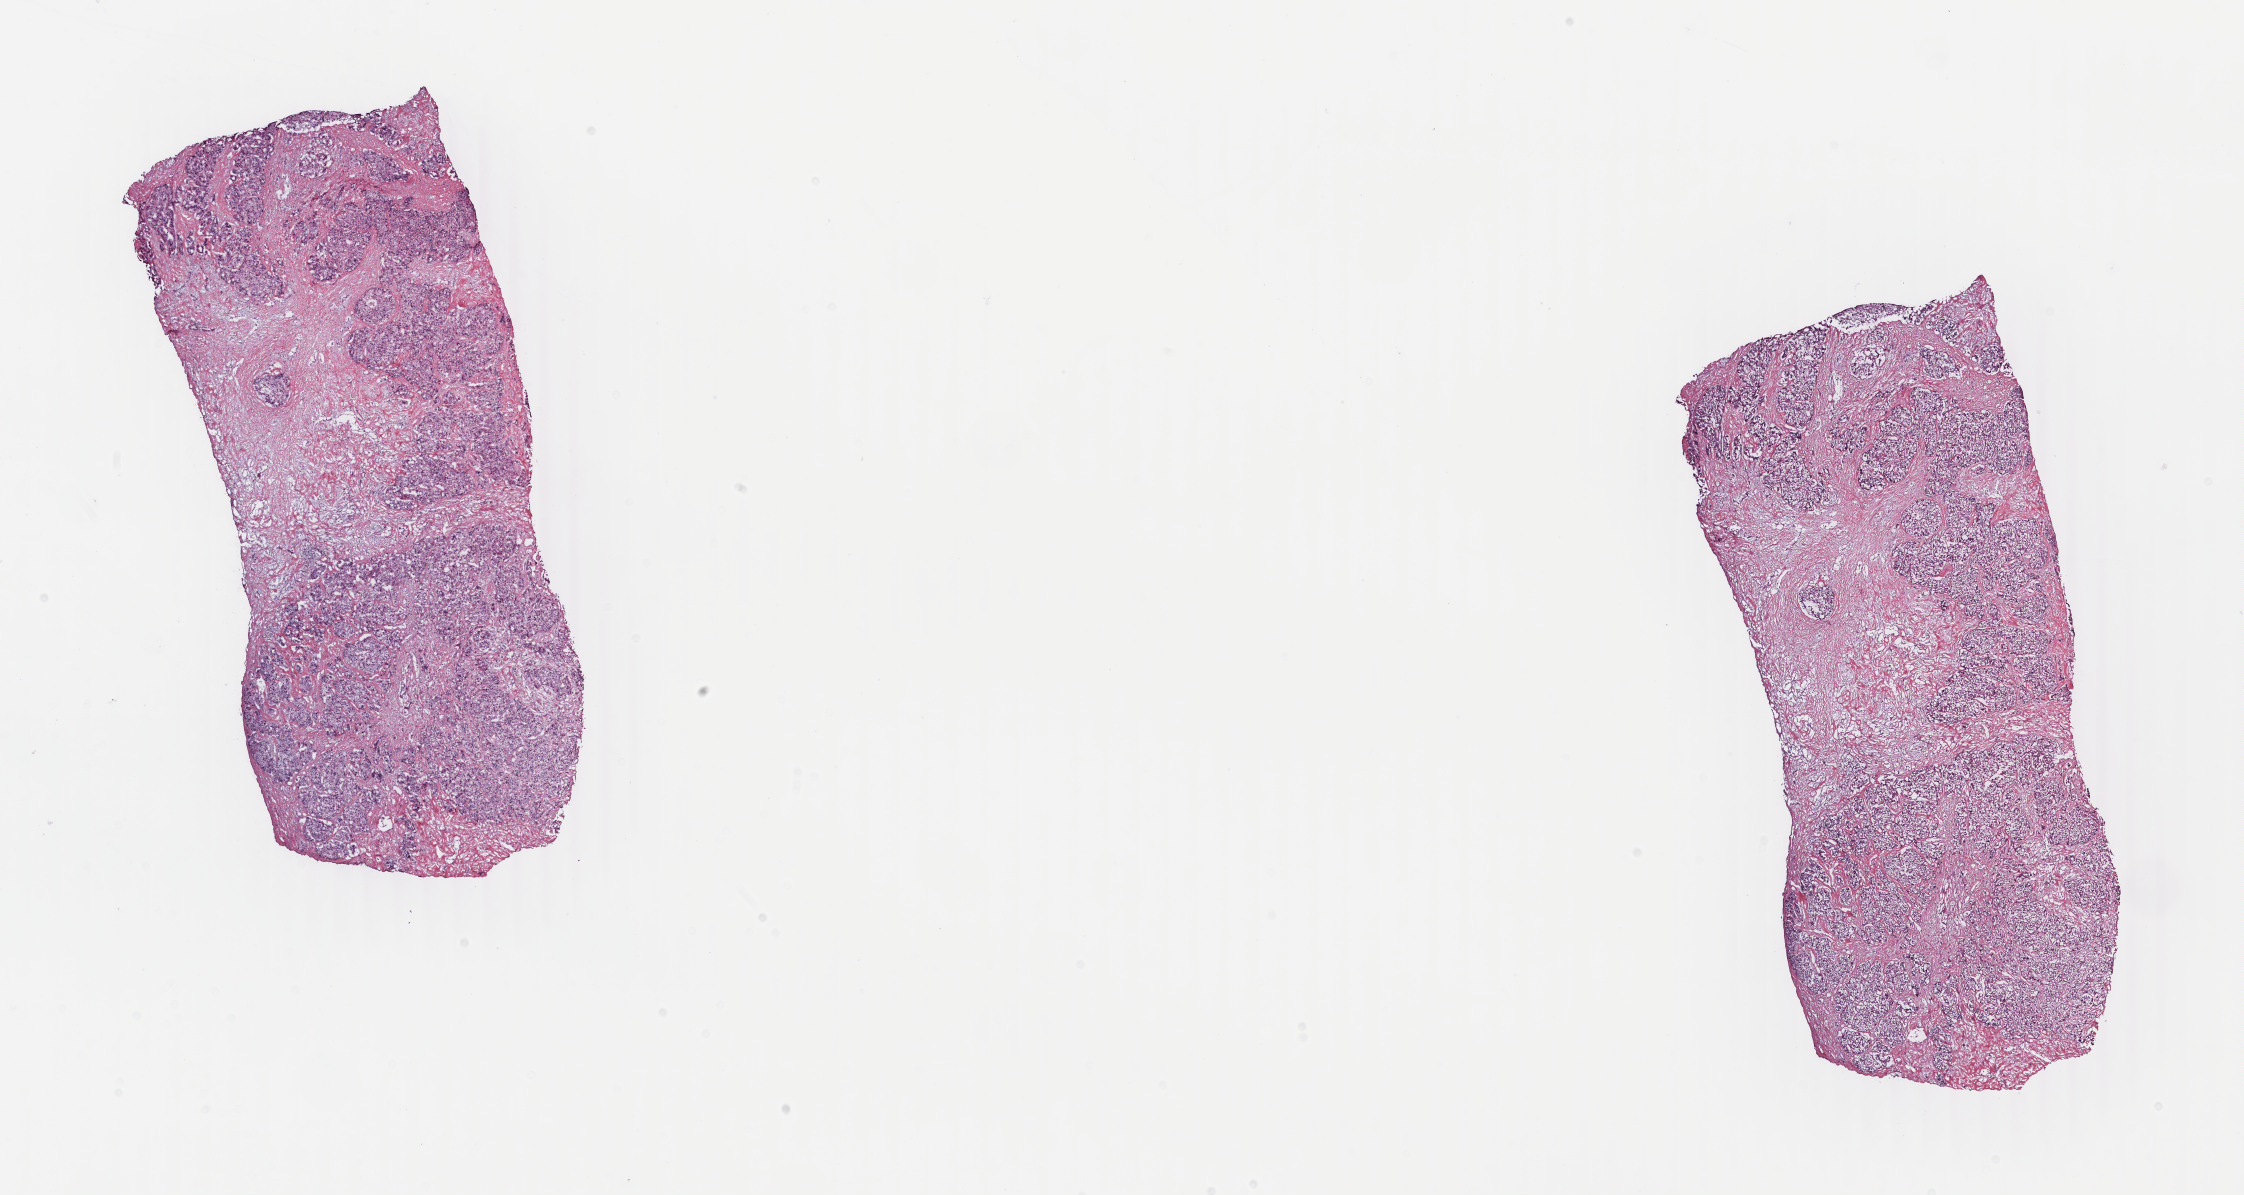
Whole-slide histology image, Hematoxylin and eosin (H&E) stained — a low-resolution overview of the entire scanned area, about 17.8 x 9.5 mm; frozen section from the top of the tissue portion; primary tumour sample from the liver. Patient: male, age at initial diagnosis 42 years. Histologic grade: G3 (poorly differentiated). Pathologist review of this section (percent, as recorded): tumour cells 65%, tumour nuclei 60%, normal cells 0%, stromal cells 35%, necrosis 0%. Inflammatory infiltration, as recorded: lymphocyte infiltration 1%, monocyte infiltration 0%, neutrophil infiltration 0%.
AJCC pathologic stage: II. Histologic diagnosis: Hepatocellular carcinoma, clear cell type.